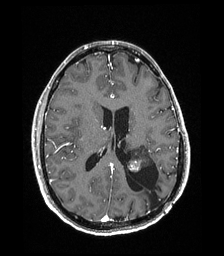
Brain MRI from a brain-tumour surgery series, one axial slice; position 84 of 192 along the scan axis; T1-weighted post-contrast; 224 × 256 image matrix, field of view 224 × 256 mm. From the clinical record (not read from this slice): histopathology: Low grade glioma; IDH mutation: no; tumour location: Left Parieto-Occipital Intraventricular.
Annotated regions visible in this slice (manually delineated by an expert):
- previous resection cavity: bounding box [x1, y1, x2, y2] px = [126, 164, 164, 208]
- tumour: [127, 145, 153, 172]